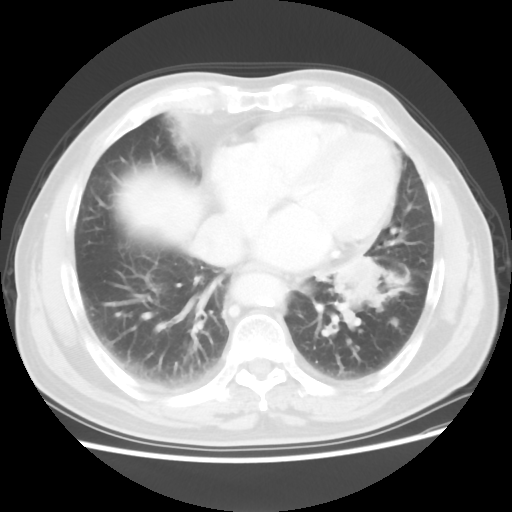
Chest CT, one axial slice; slice 23 of 56 in the series (ordered by position); lung window (W 1500 / L -600 HU); 5 mm slice thickness; 512 × 512 image matrix, field of view 360 × 360 mm. Male patient, age 75 years. From the clinical record (not read from this slice): clinical TNM (as recorded): T3 N0 M0.
Structures marked on this image (bounding box drawn by a radiologist):
- lung tumour (recorded histology: squamous cell carcinoma): bounding box <328,246,393,324> (left, top, right, bottom; pixels)